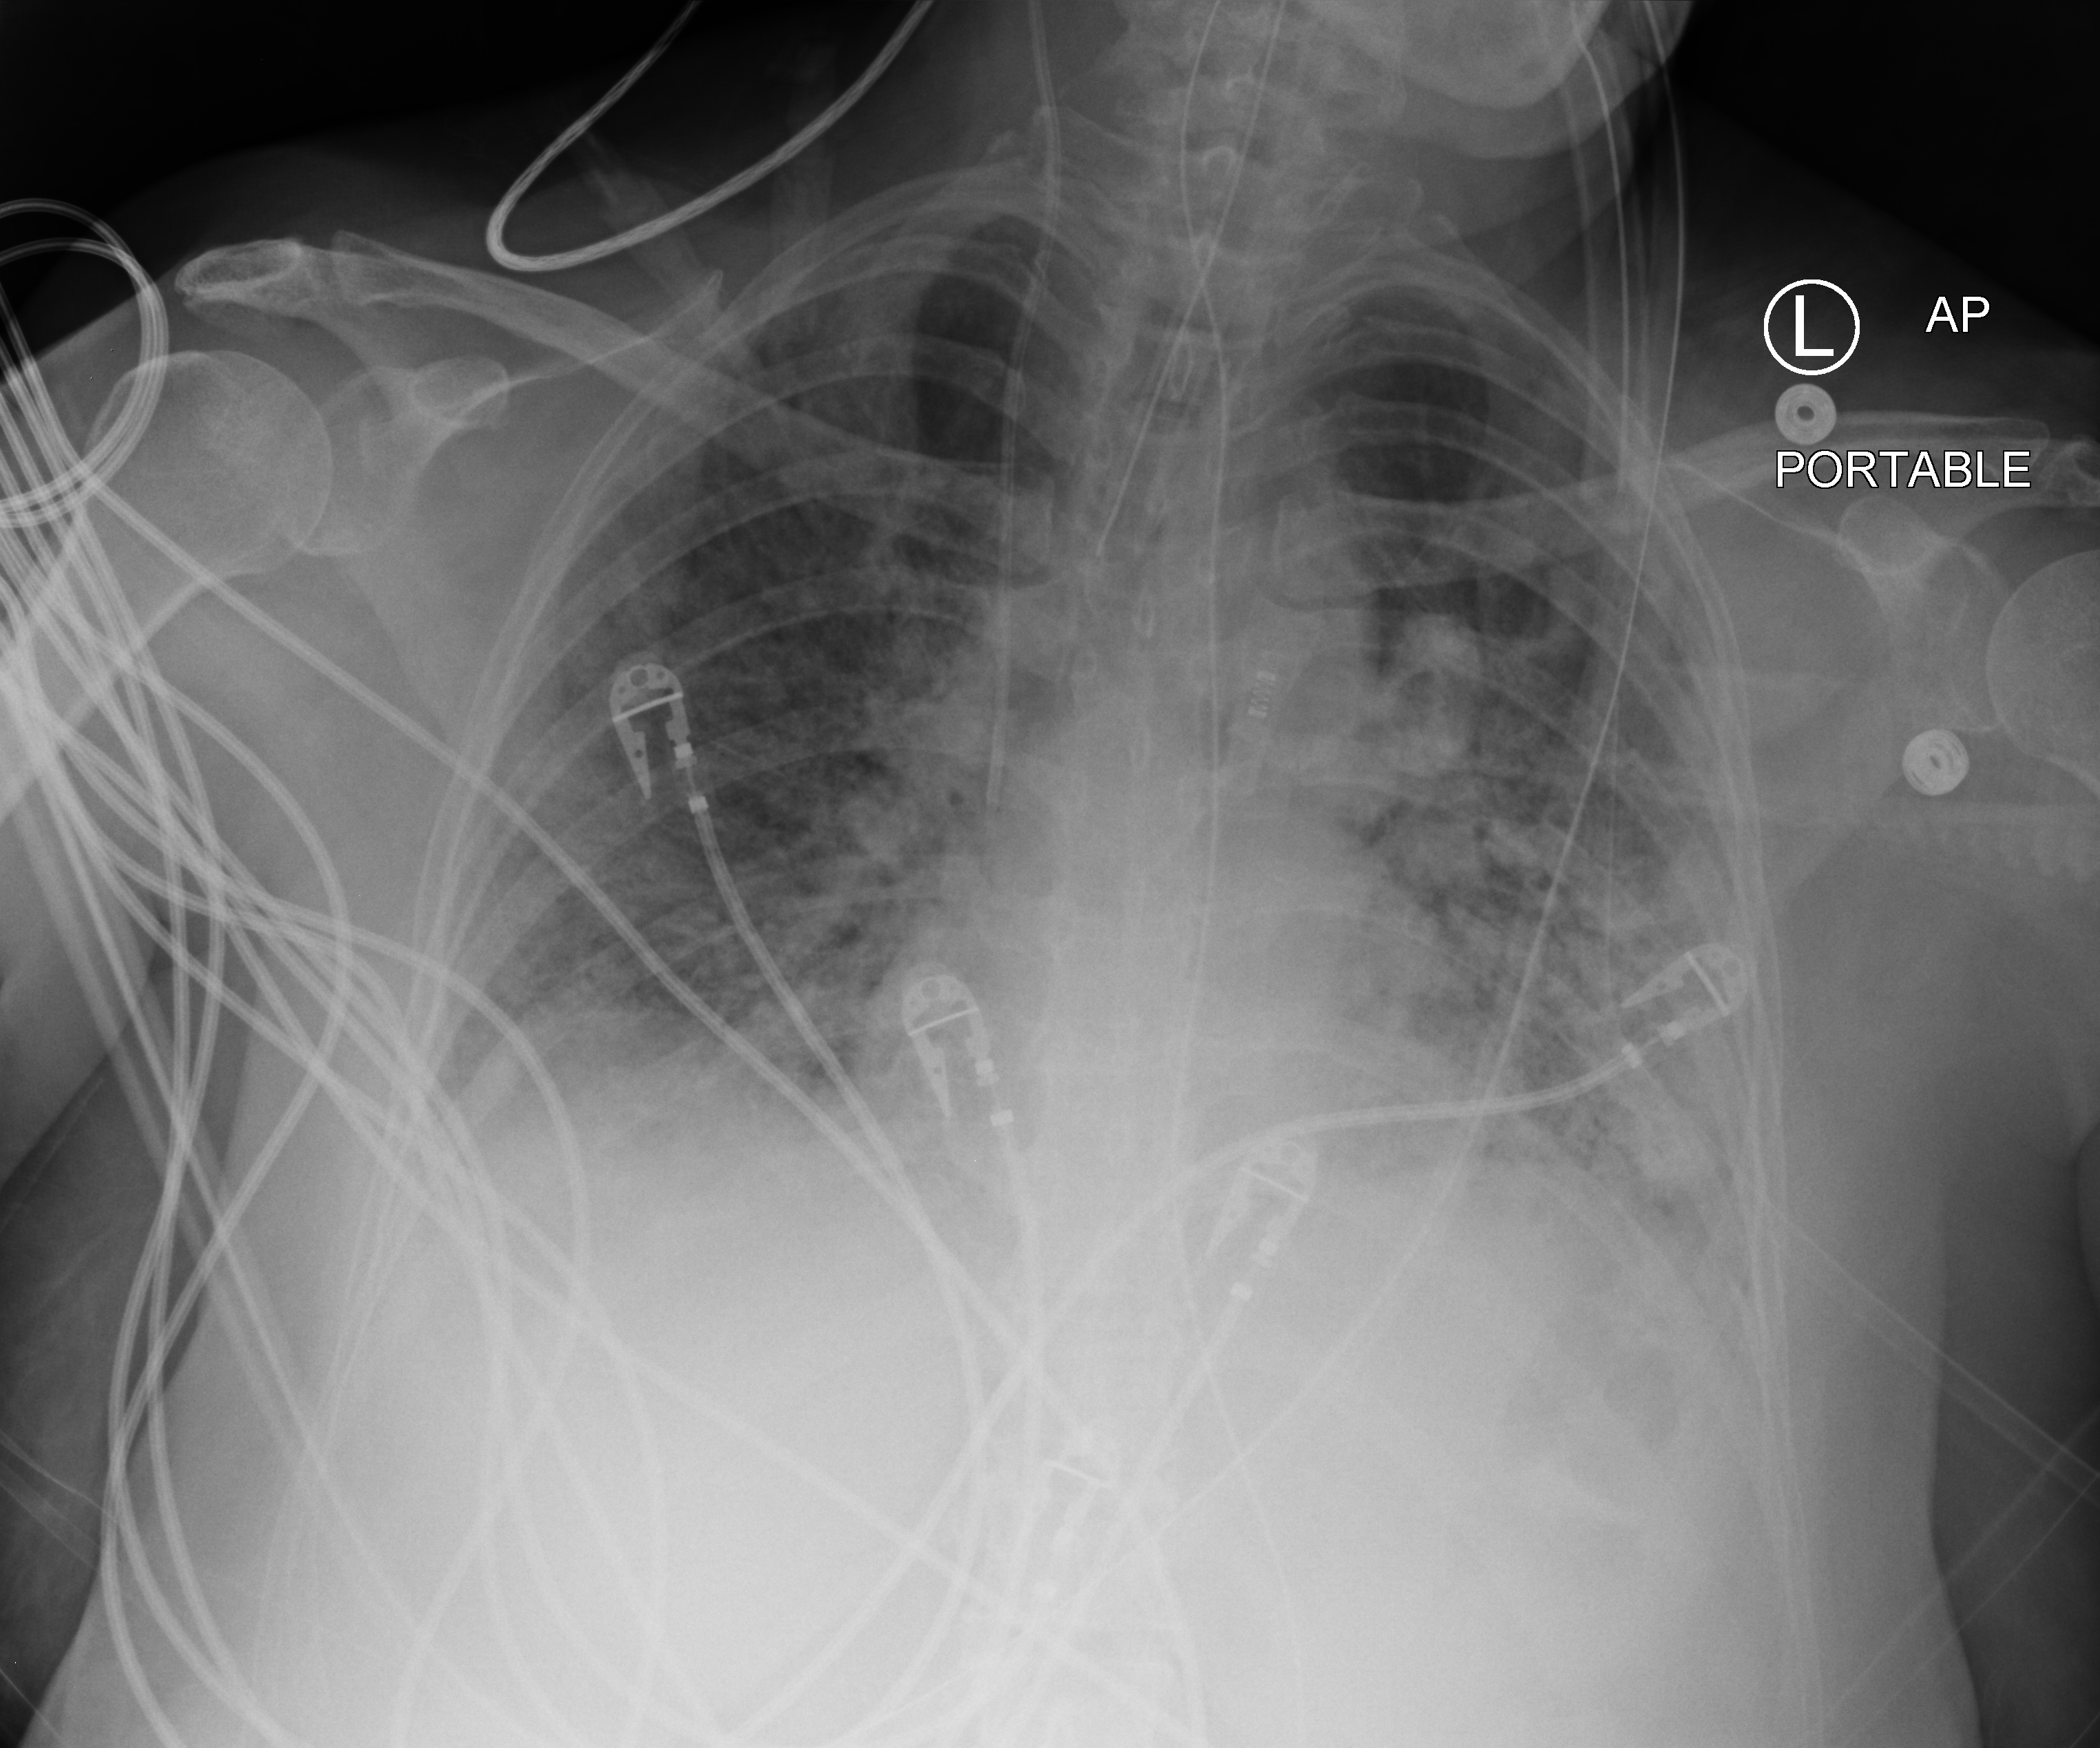
Bedside chest radiograph (computed radiography), anteroposterior (AP) projection. Patient hospitalised with COVID-19; female, aged 60–74 years.
Hospital-stay facts (about this admission, not read from this image; timing relative to this image not recorded):
- admitted to intensive care during this hospital stay: yes
- mechanically ventilated during this hospital stay: yes
- hypertension (admission record): yes